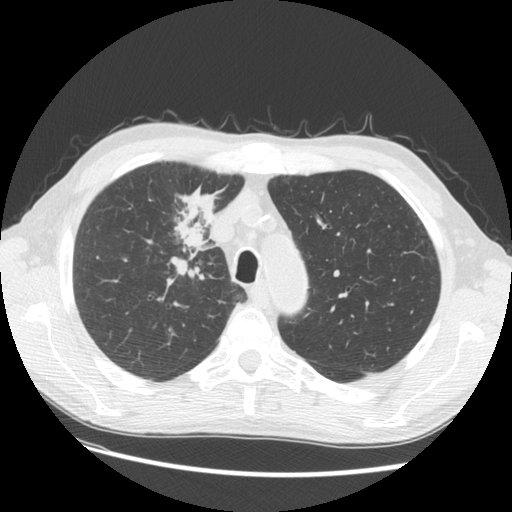
Axial slice from a low-dose chest CT screening exam. Third annual screen. Lung window (W 1500 / L -600 HU). 2.5 mm slice thickness. Standard (soft-tissue) reconstruction kernel (STANDARD). 120 kVp. Male participant, aged 73 years at enrolment.
Expert-annotated lung lesion, box from (x=142, y=181) to (x=232, y=279) px. The screening reader recorded 4 non-calcified nodules or masses ≥4 mm on this exam (right upper lobe, right upper lobe, right upper lobe, left lower lobe); which of them this box marks is not recorded. Official screen result: positive, other. Later outcome: lung cancer diagnosed 48 days after this screen — squamous cell carcinoma, NOS, right upper lobe, poorly differentiated (G3), stage IIIB (AJCC 6th edition), 56 mm at pathology.